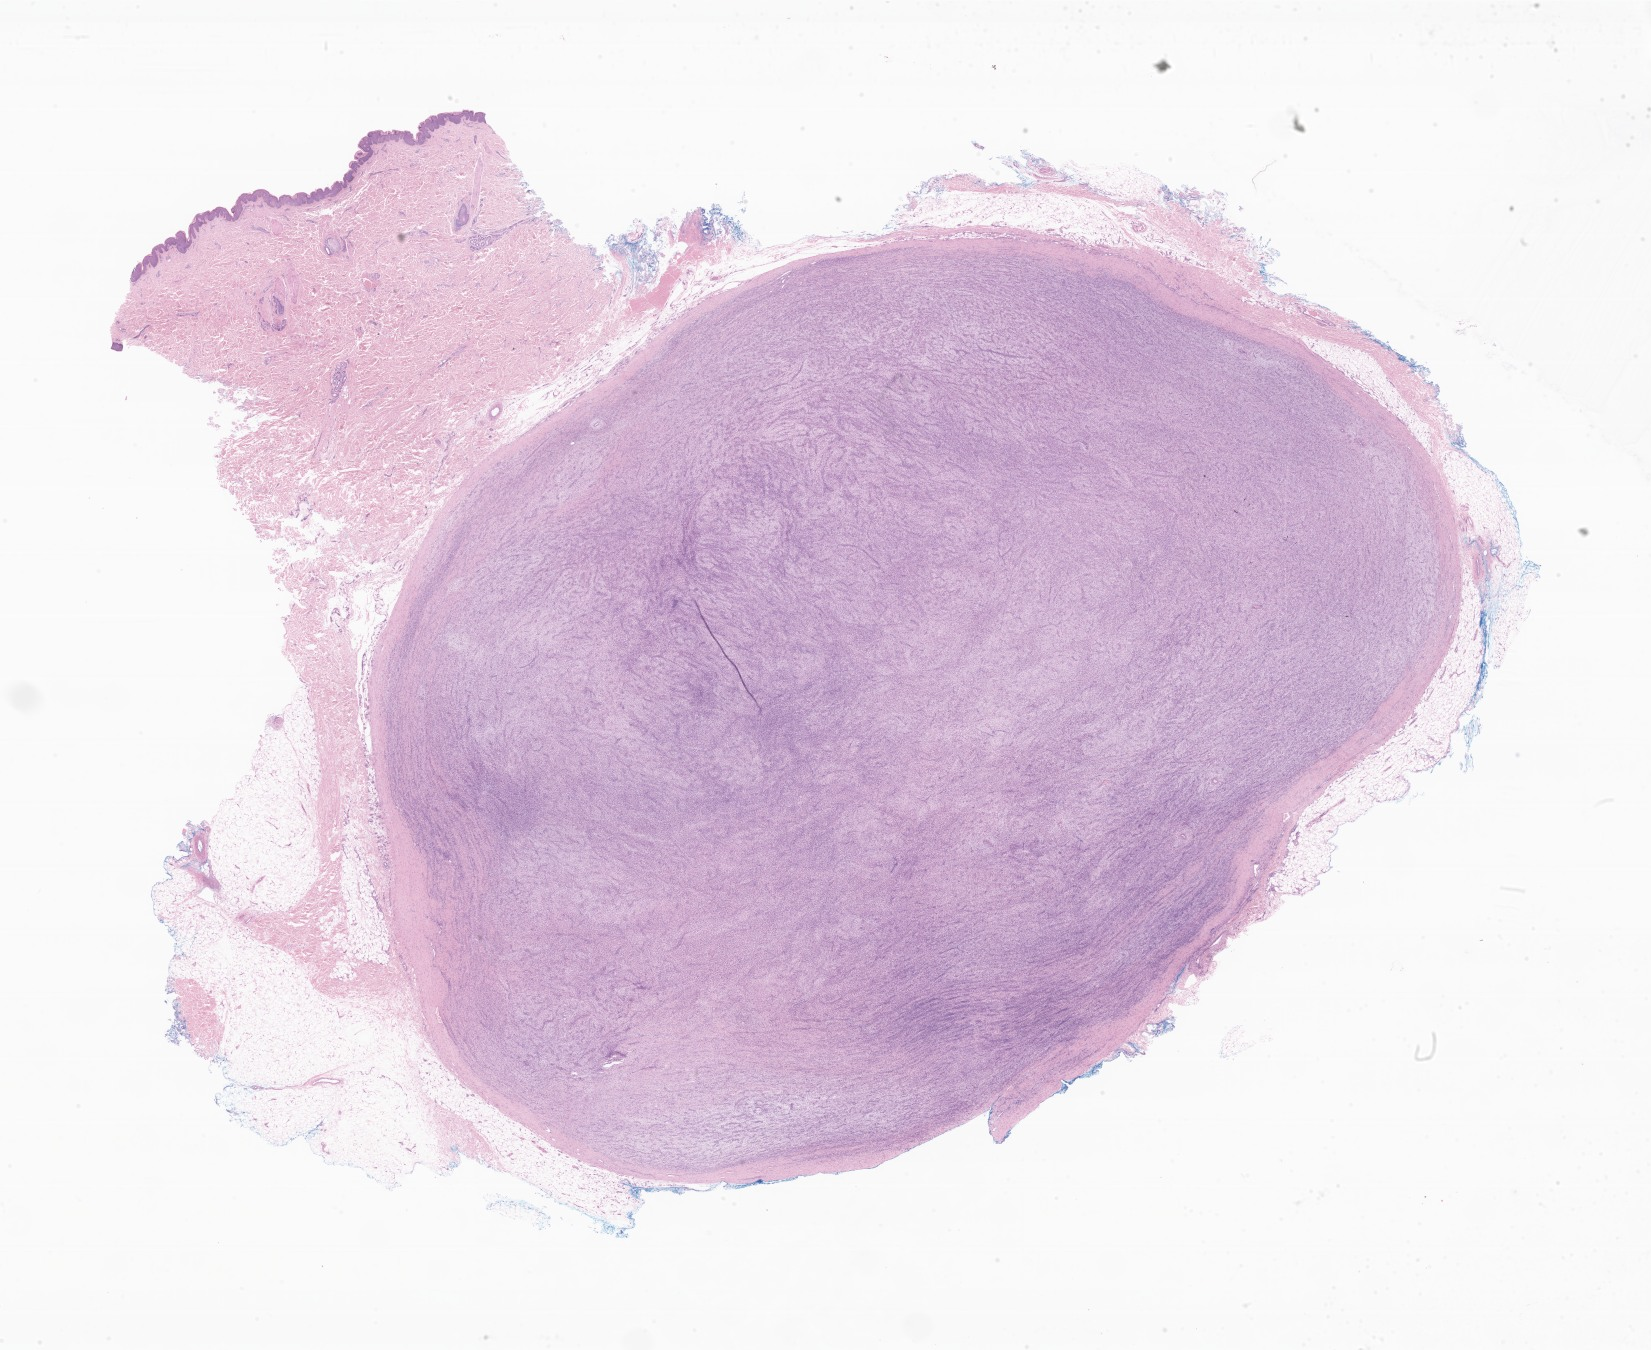
Haematoxylin and eosin whole-slide image of tumor tissue from the skin of lower limb — whole scanned area (about 27.8 x 22.8 mm) shown as a low-resolution overview; FFPE section. Patient male; age 188 months (15 years 8 months).
Diagnosis: Myxofibrosarcoma.